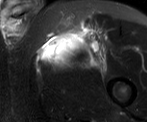
MRI of an extremity soft-tissue mass, one axial slice. T2-weighted fat-saturated. MR volume resampled by the dataset authors to the PET/CT grid (not the native acquisition matrix). 147 × 122 image matrix, field of view 144 × 119 mm. Male patient. Case-level facts recorded for this patient, not image findings: histological type: pleiomorphic liposarcoma; grade: high; site of the primary tumour: left thigh.
Structures marked on this image (expert contour drawn on MRI and transferred to this co-registered scan by the dataset authors):
- gross tumour volume including surrounding oedema: bounding box (x1, y1, x2, y2) in pixels: (41, 28, 102, 63)
- gross tumour volume (mass): (41, 35, 76, 61)